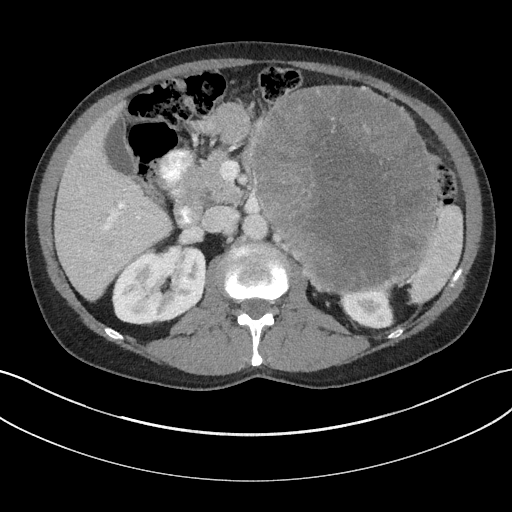
Contrast-enhanced abdominal CT, one axial slice. Position 103 of 147 along the scan axis. Reconstruction kernel I31f/3. Intravenous contrast given. Soft-tissue window (W 400 / L 40 HU). 512 × 512 image matrix, field of view 384 × 384 mm. Male patient, age 58 years. From the clinical record (not read from this slice): diagnosis: adrenocortical carcinoma; tumour side: left adrenal; tumour size at pathology: 22 cm; Ki-67 index: 26 %; stage (as recorded): 2.
Outlined on this slice (semi-automatically segmented with operator editing):
- mass: bounding box (x1, y1, x2, y2) in pixels: (254, 86, 435, 291)